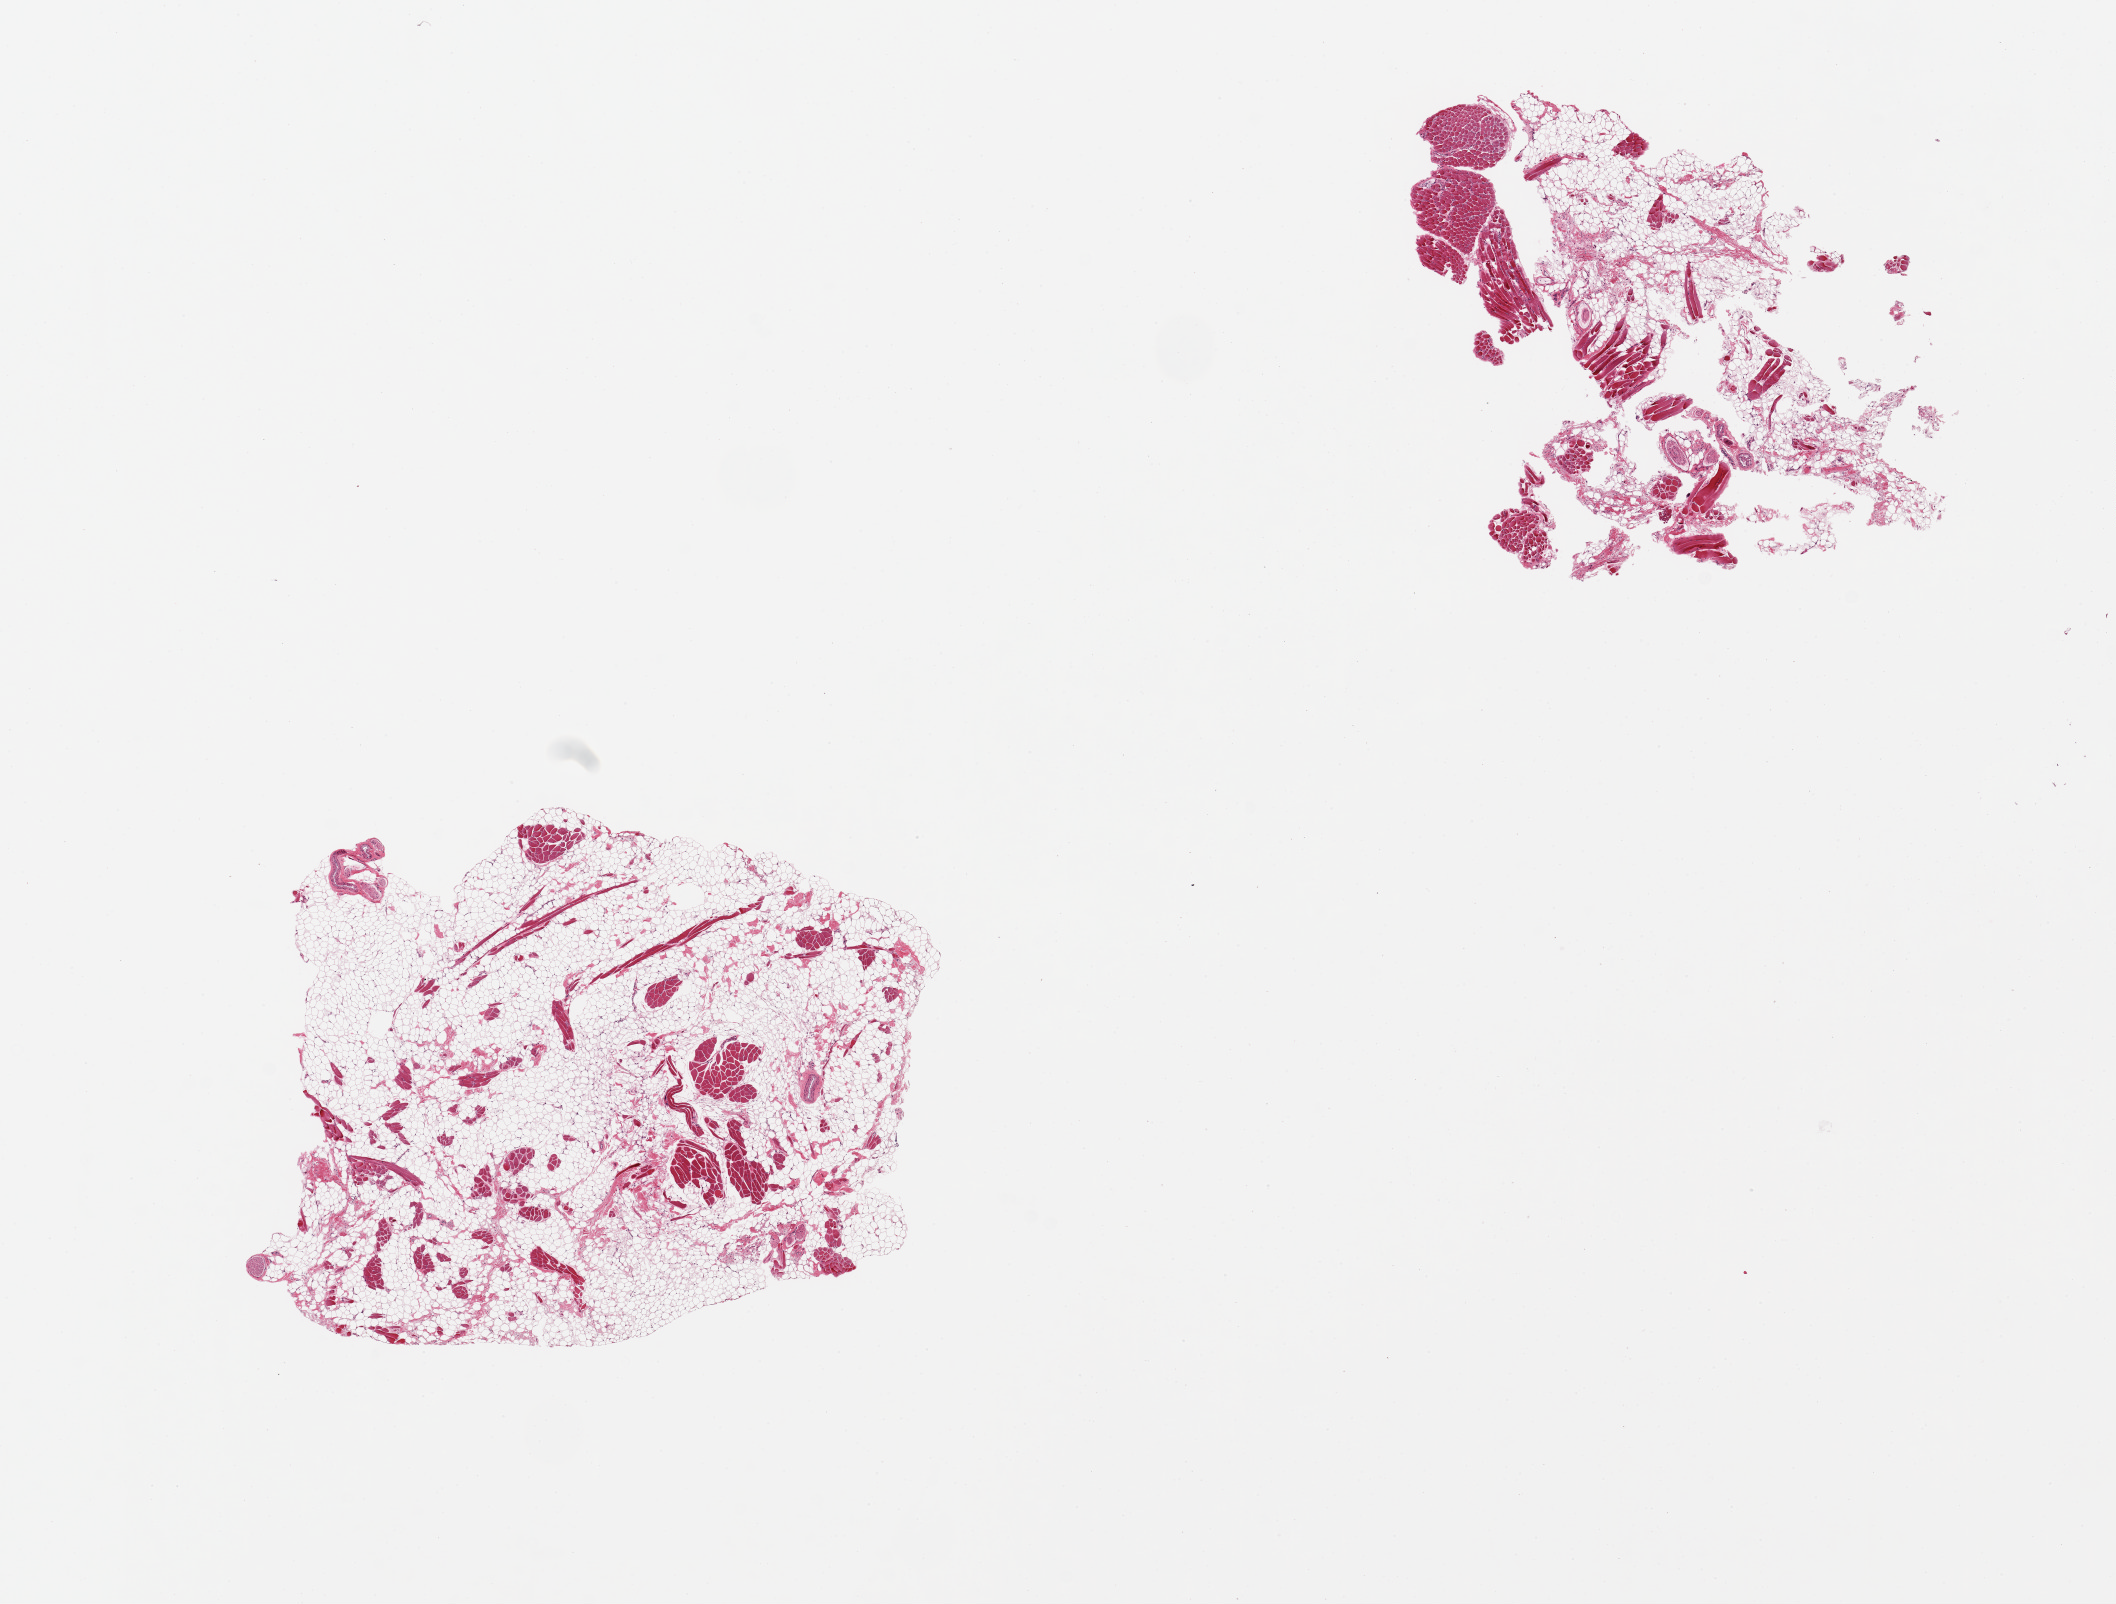
Digitized hematoxylin and eosin (H&E)-stained section — shown as a low-resolution overview of the whole scanned area (about 16.7 x 12.7 mm); PAXgene-fixed paraffin-embedded (PFPE) section; target tissue: minor salivary gland; donor tissue sample. Donor sex: female.
Pathologist's review note for this sample: 2 pieces, fat/skeletal muscle fibers only, no glandular tissue.